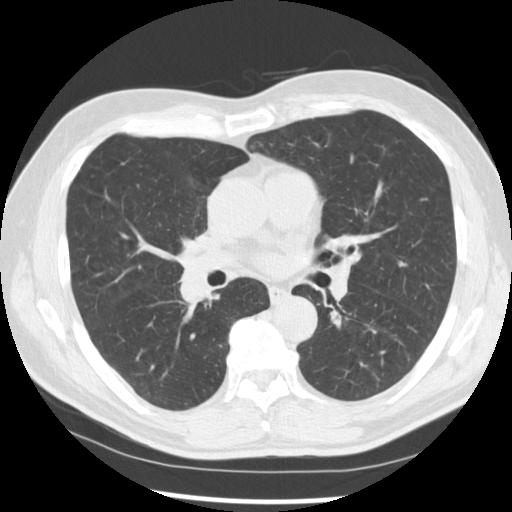
Low-dose screening chest CT, axial slice. Baseline screening round. Lung window (W 1500 / L -600 HU). 2.5 mm slice thickness. Standard (soft-tissue) reconstruction kernel (STANDARD). 512 × 512 image matrix. Male, age 67 years at enrolment. Current smoker at enrolment.
- Lesion marked by an expert reader, box from (x=160, y=248) to (x=229, y=312) px.
- Screening reader's record for this exam (one nodule recorded; not confirmed to be the boxed lesion): non-calcified nodule or mass ≥4 mm, left lower lobe, 15 × 15 mm, spiculated (stellate) margins, soft tissue attenuation.
- Note: the box lies in the patient's right hemithorax on this image, whereas the reader's record names the left lung; they may be different findings.
- Official screen result: positive, change unspecified: nodule(s) >= 4 mm or enlarging nodule(s), mass(es), or other non-specific abnormalities suspicious for lung cancer.
- Later outcome: lung cancer diagnosed 49 days after this screen — squamous cell carcinoma, NOS, right middle lobe, poorly differentiated (G3), stage IIB (AJCC 6th edition), 35 mm at pathology.